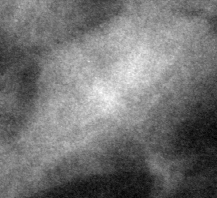
Region of interest cut from a scanned film mammogram (one marked finding), left breast, CC view.
Finding: mass, shape lobulated, margins circumscribed; BI-RADS assessment category 3; pathology (as recorded): benign.